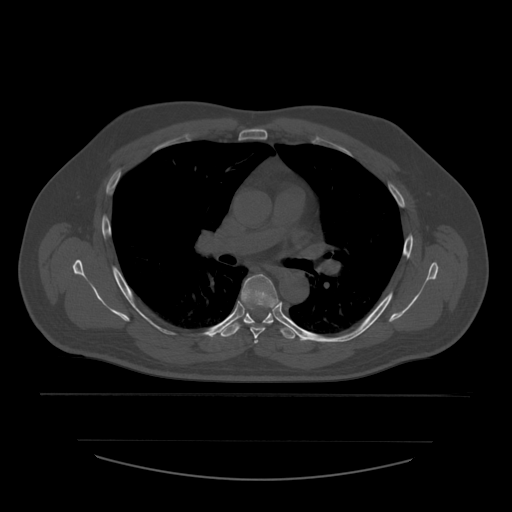
CT including the spine, one axial slice; position 389 of 532 along the scan axis; 120 kVp; bone window (W 1800 / L 400 HU); 1.25 mm slice thickness; 512 × 512 image matrix, field of view 441 × 441 mm. Patient age 44 years. From the clinical record (not read from this slice): primary cancer: soft tissue sarcoma.
Annotated regions visible in this slice (semi-automatic segmentation, software-assisted and operator-edited):
- T4 vertebra: box from (x=254, y=339) to (x=259, y=344) px
- T5 vertebra: (x=241, y=274)–(x=279, y=339)
- T6 vertebra: (x=221, y=303)–(x=298, y=340)